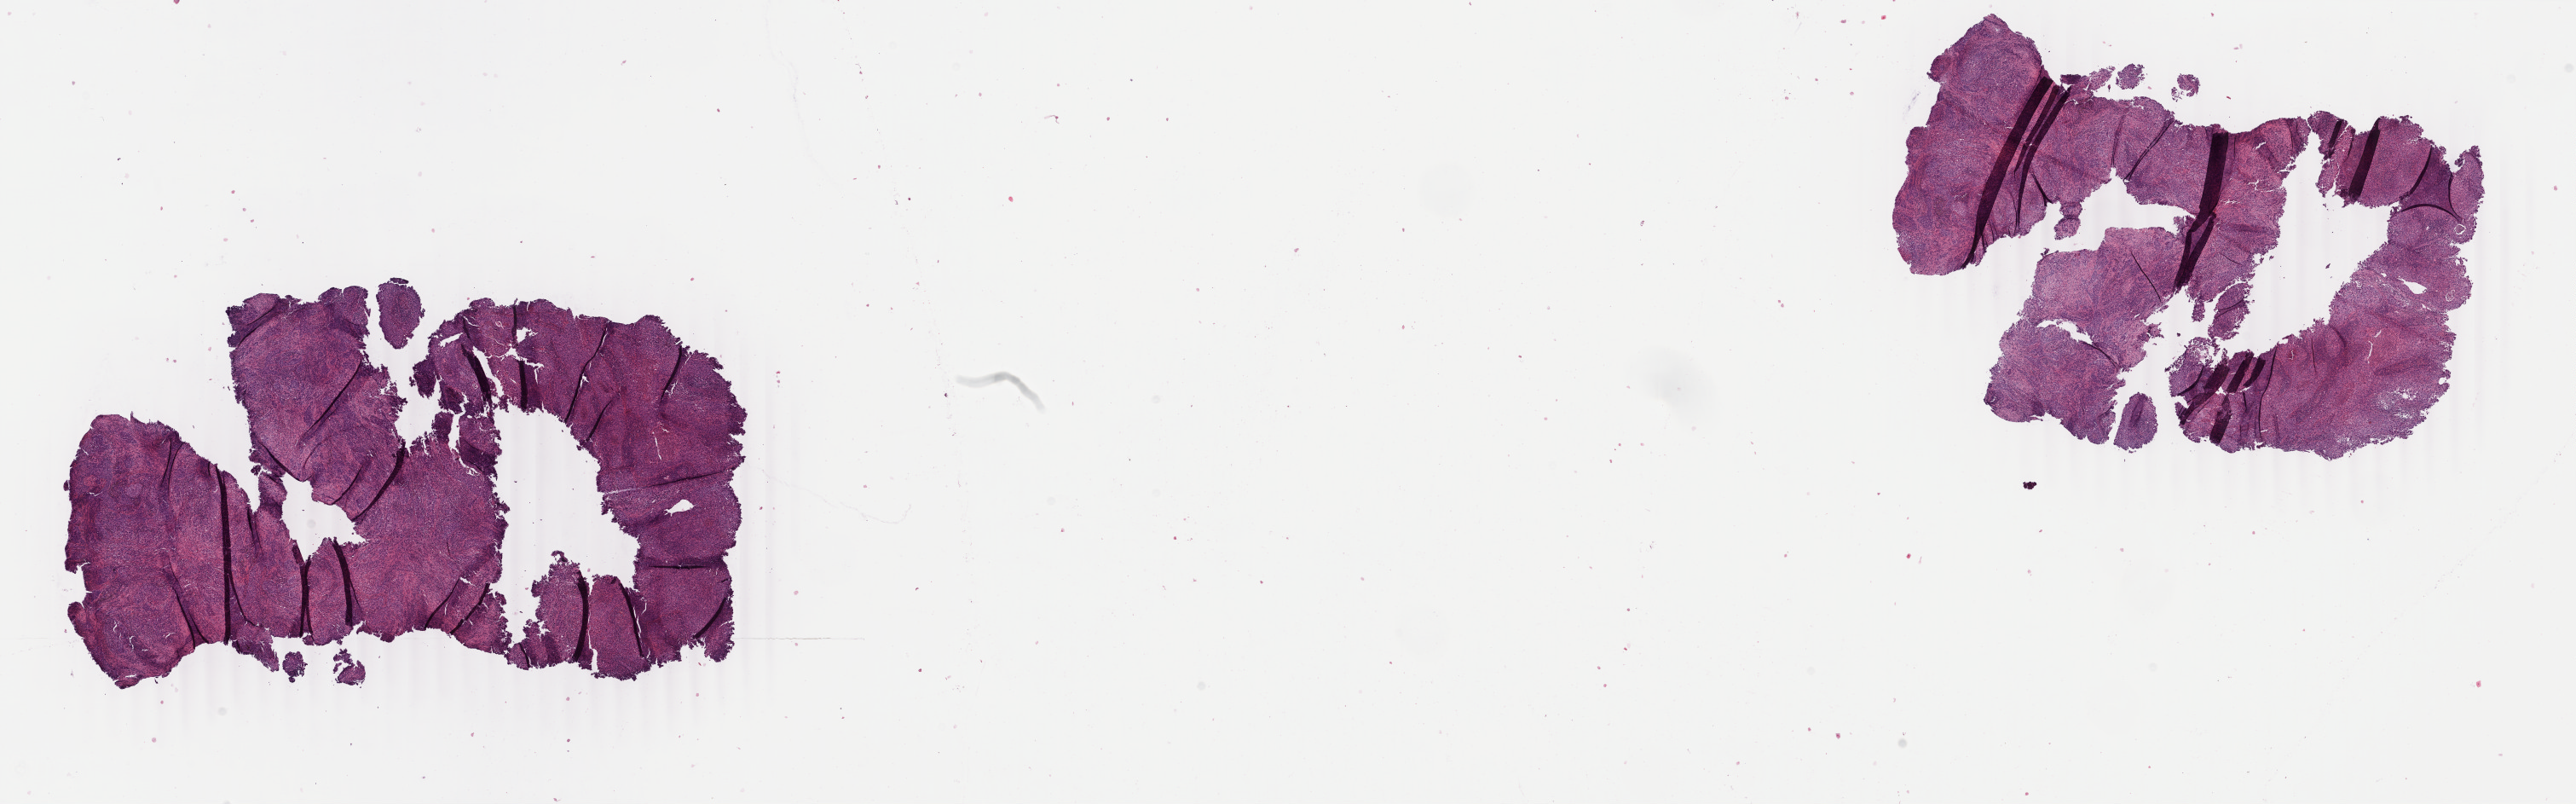
Hematoxylin and eosin (H&E) stained whole-slide image, a low-resolution overview of the entire scanned area, about 24.0 x 7.5 mm (slide scanned at 40x); formalin-fixed paraffin-embedded (FFPE) diagnostic section; lung, primary tumour sample. Female, age 61 years at initial diagnosis.
* laterality: right
* AJCC pathologic stage: IIA (7th edition)
* pathologic diagnosis: Squamous cell carcinoma, NOS (upper lobe, lung)